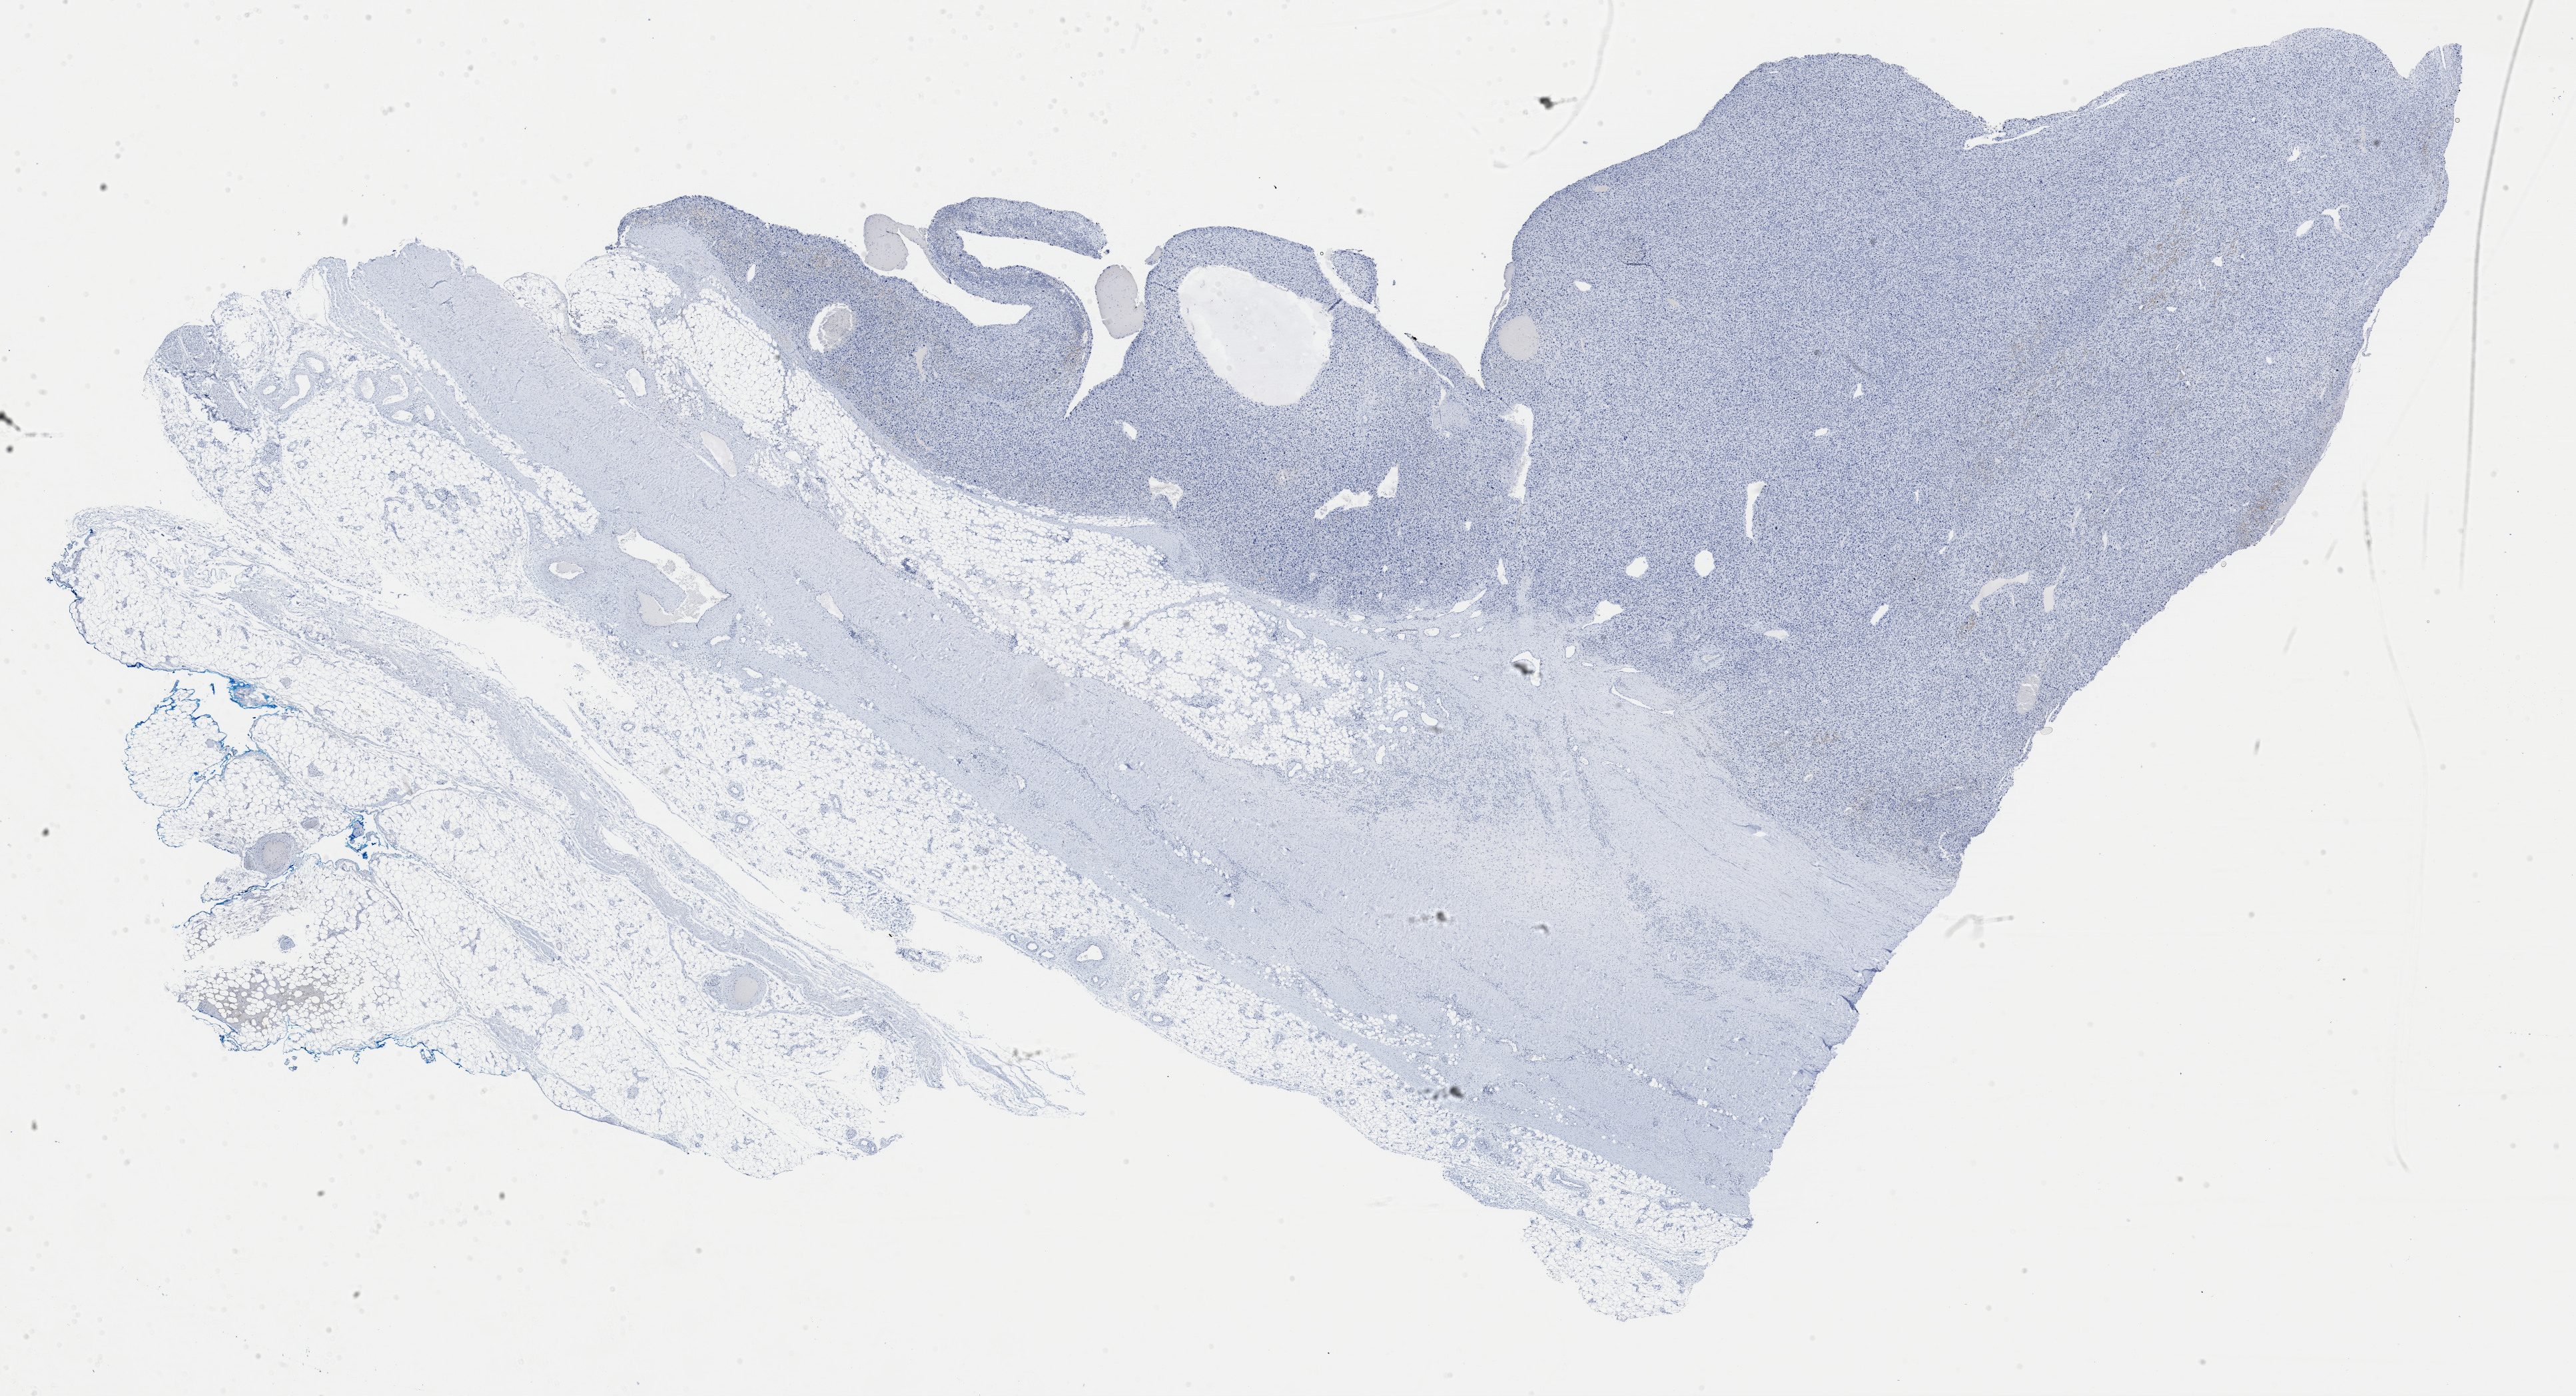
Whole-slide histology image, H&E-stained, a low-resolution overview of the entire scanned area, about 30.5 x 16.5 mm (from a 40x scan); formalin-fixed paraffin-embedded (FFPE) diagnostic section; sample: primary tumour, connective, subcutaneous and other soft tissues. Female, age 75 years at initial diagnosis.
• histologic diagnosis: Malignant fibrous histiocytoma (connective, subcutaneous and other soft tissues of lower limb and hip)